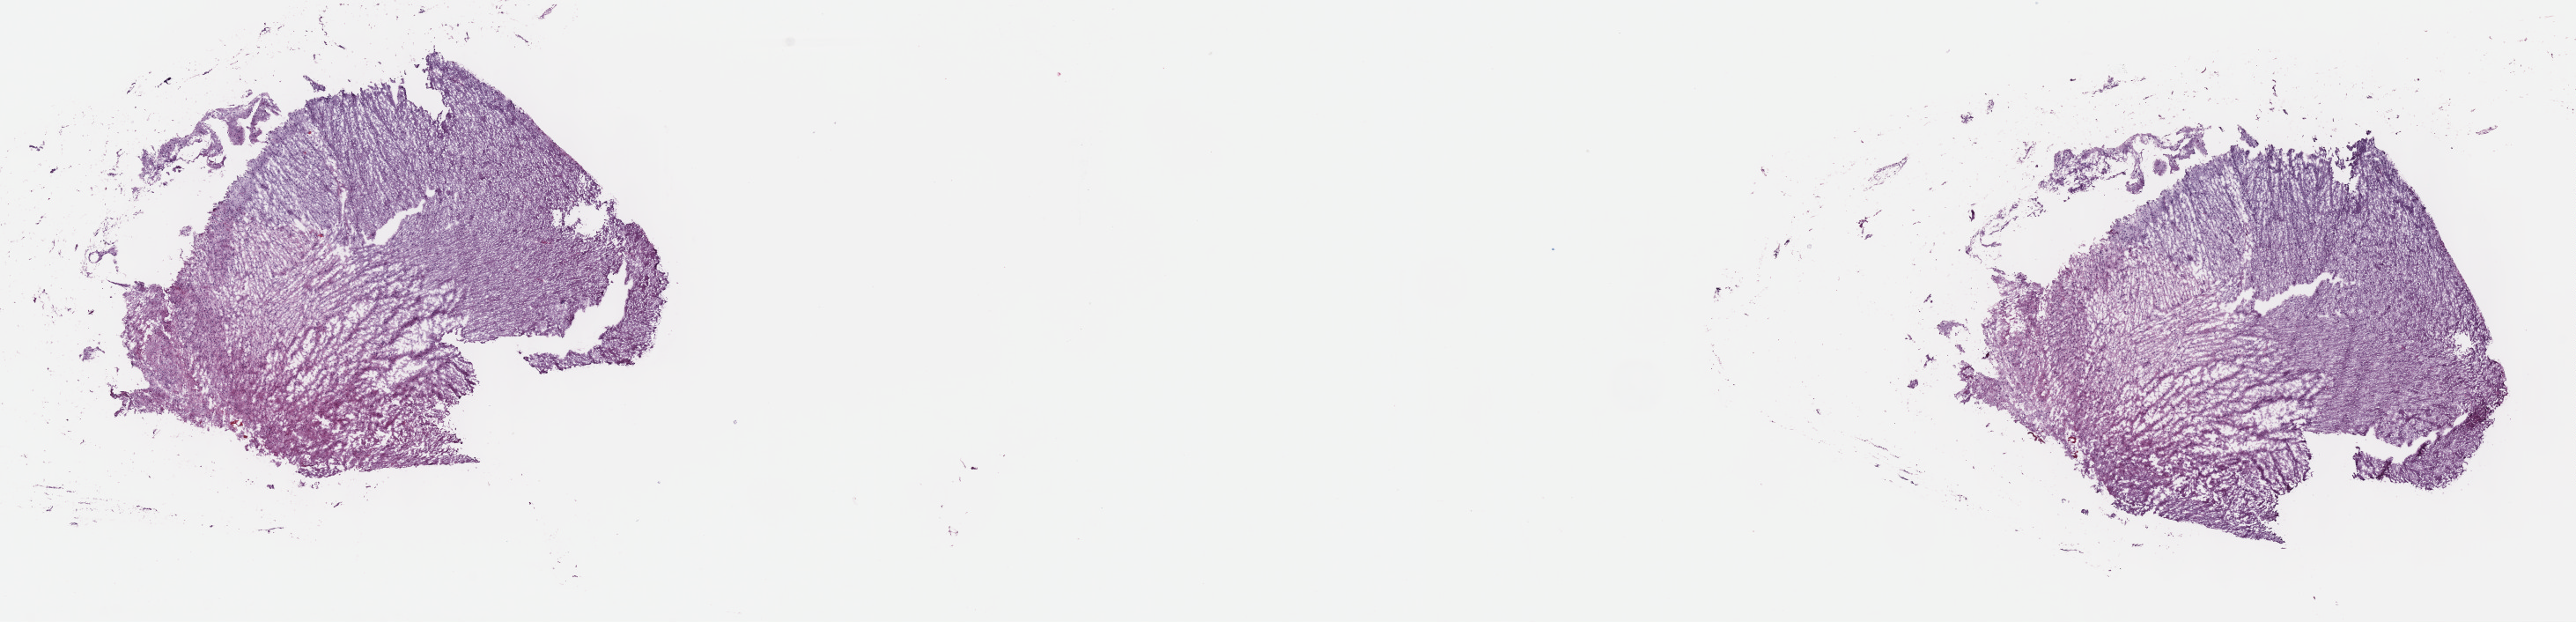
Hematoxylin and eosin (H&E) stained whole-slide image — shown as a low-resolution overview of the whole scanned area (about 23.7 x 5.7 mm). Frozen section. Brain, primary tumour sample. Patient: male, age at initial diagnosis 32 years. Histologic grade: G2 (moderately differentiated). Composition of this section per pathologist review: tumour cells 50%, tumour nuclei 70%, normal cells 10%, stromal cells 40%, necrosis 0%. Infiltration values recorded for this section: lymphocyte infiltration 0%, monocyte infiltration 0%, neutrophil infiltration 0%.
• laterality: right
• pathologic diagnosis: Astrocytoma, NOS (cerebrum)